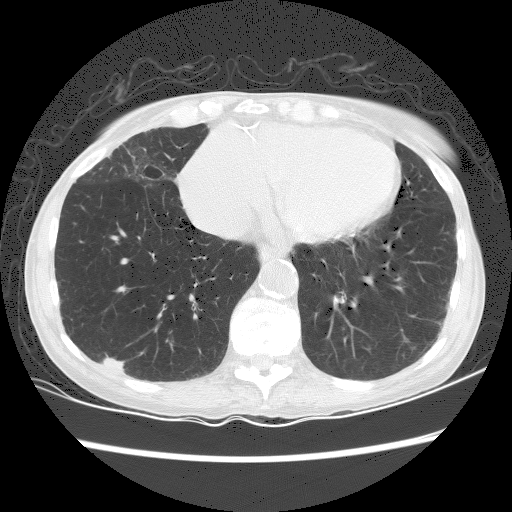
Chest CT (low-dose screening protocol), one axial image; first (baseline) screen; lung window (W 1500 / L -600 HU); 2.5 mm slice thickness; lung (sharp) reconstruction kernel (BONE); 120 kVp; slice 97 of 156 in the series. Female, age 70 years at enrolment.
Expert reader's lesion annotation, box from (x=90, y=345) to (x=141, y=385) px. The screening reader recorded 2 non-calcified nodules or masses ≥4 mm on this exam (right lower lobe, left lower lobe); which of them this box marks is not recorded. Participant outcome: lung cancer diagnosed 125 days after this screen — squamous cell carcinoma, NOS, right lower lobe, well differentiated (G1), stage IA (AJCC 6th edition), 25 mm at pathology.